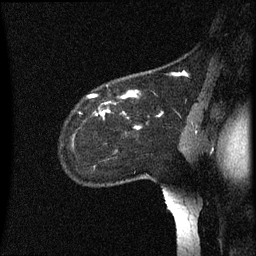
Breast MRI (dynamic contrast-enhanced), one sagittal slice; slice 48 of 60 in the series (ordered by position); dynamic contrast-enhanced series, image 2 of 3 at this slice position (ordered by acquisition); 1.5 T; TE 4.2 ms, TR 8.4 ms; 2.2 mm slice thickness; 256 × 256 image matrix, field of view 200 × 200 mm. Female patient, age 35 years. Case-level facts recorded for this patient, not image findings: setting: breast cancer imaged before/during neoadjuvant chemotherapy; receptor status: HER2-positive.
Structures marked on this image (semi-automatic segmentation, software-assisted and operator-edited):
- analysis volume of interest (the breast-tissue region the enhancement analysis was run in; not a lesion): box from (x=61, y=72) to (x=164, y=171) px
- tumour enhancement mask (voxels above the 70 % enhancement threshold inside the analysis volume of interest): (x=89, y=92)–(x=140, y=129)